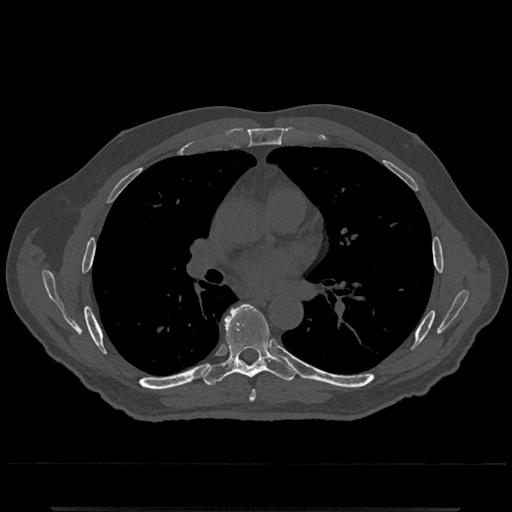
CT including the spine, one axial slice. Position 731 of 797 along the scan axis. Reconstruction kernel Br40s/3. 120 kVp. Bone window (W 1800 / L 400 HU). 0.5 mm slice thickness. 512 × 512 image matrix, field of view 393 × 393 mm. Patient: male, 67 years. Case-level facts recorded for this patient, not image findings: primary cancer: prostate.
Structures marked on this image (semi-automatically segmented with operator editing):
- T6 vertebra: bounding box <249,392,256,402> (left, top, right, bottom; pixels)
- T7 vertebra: <204,304,297,386>